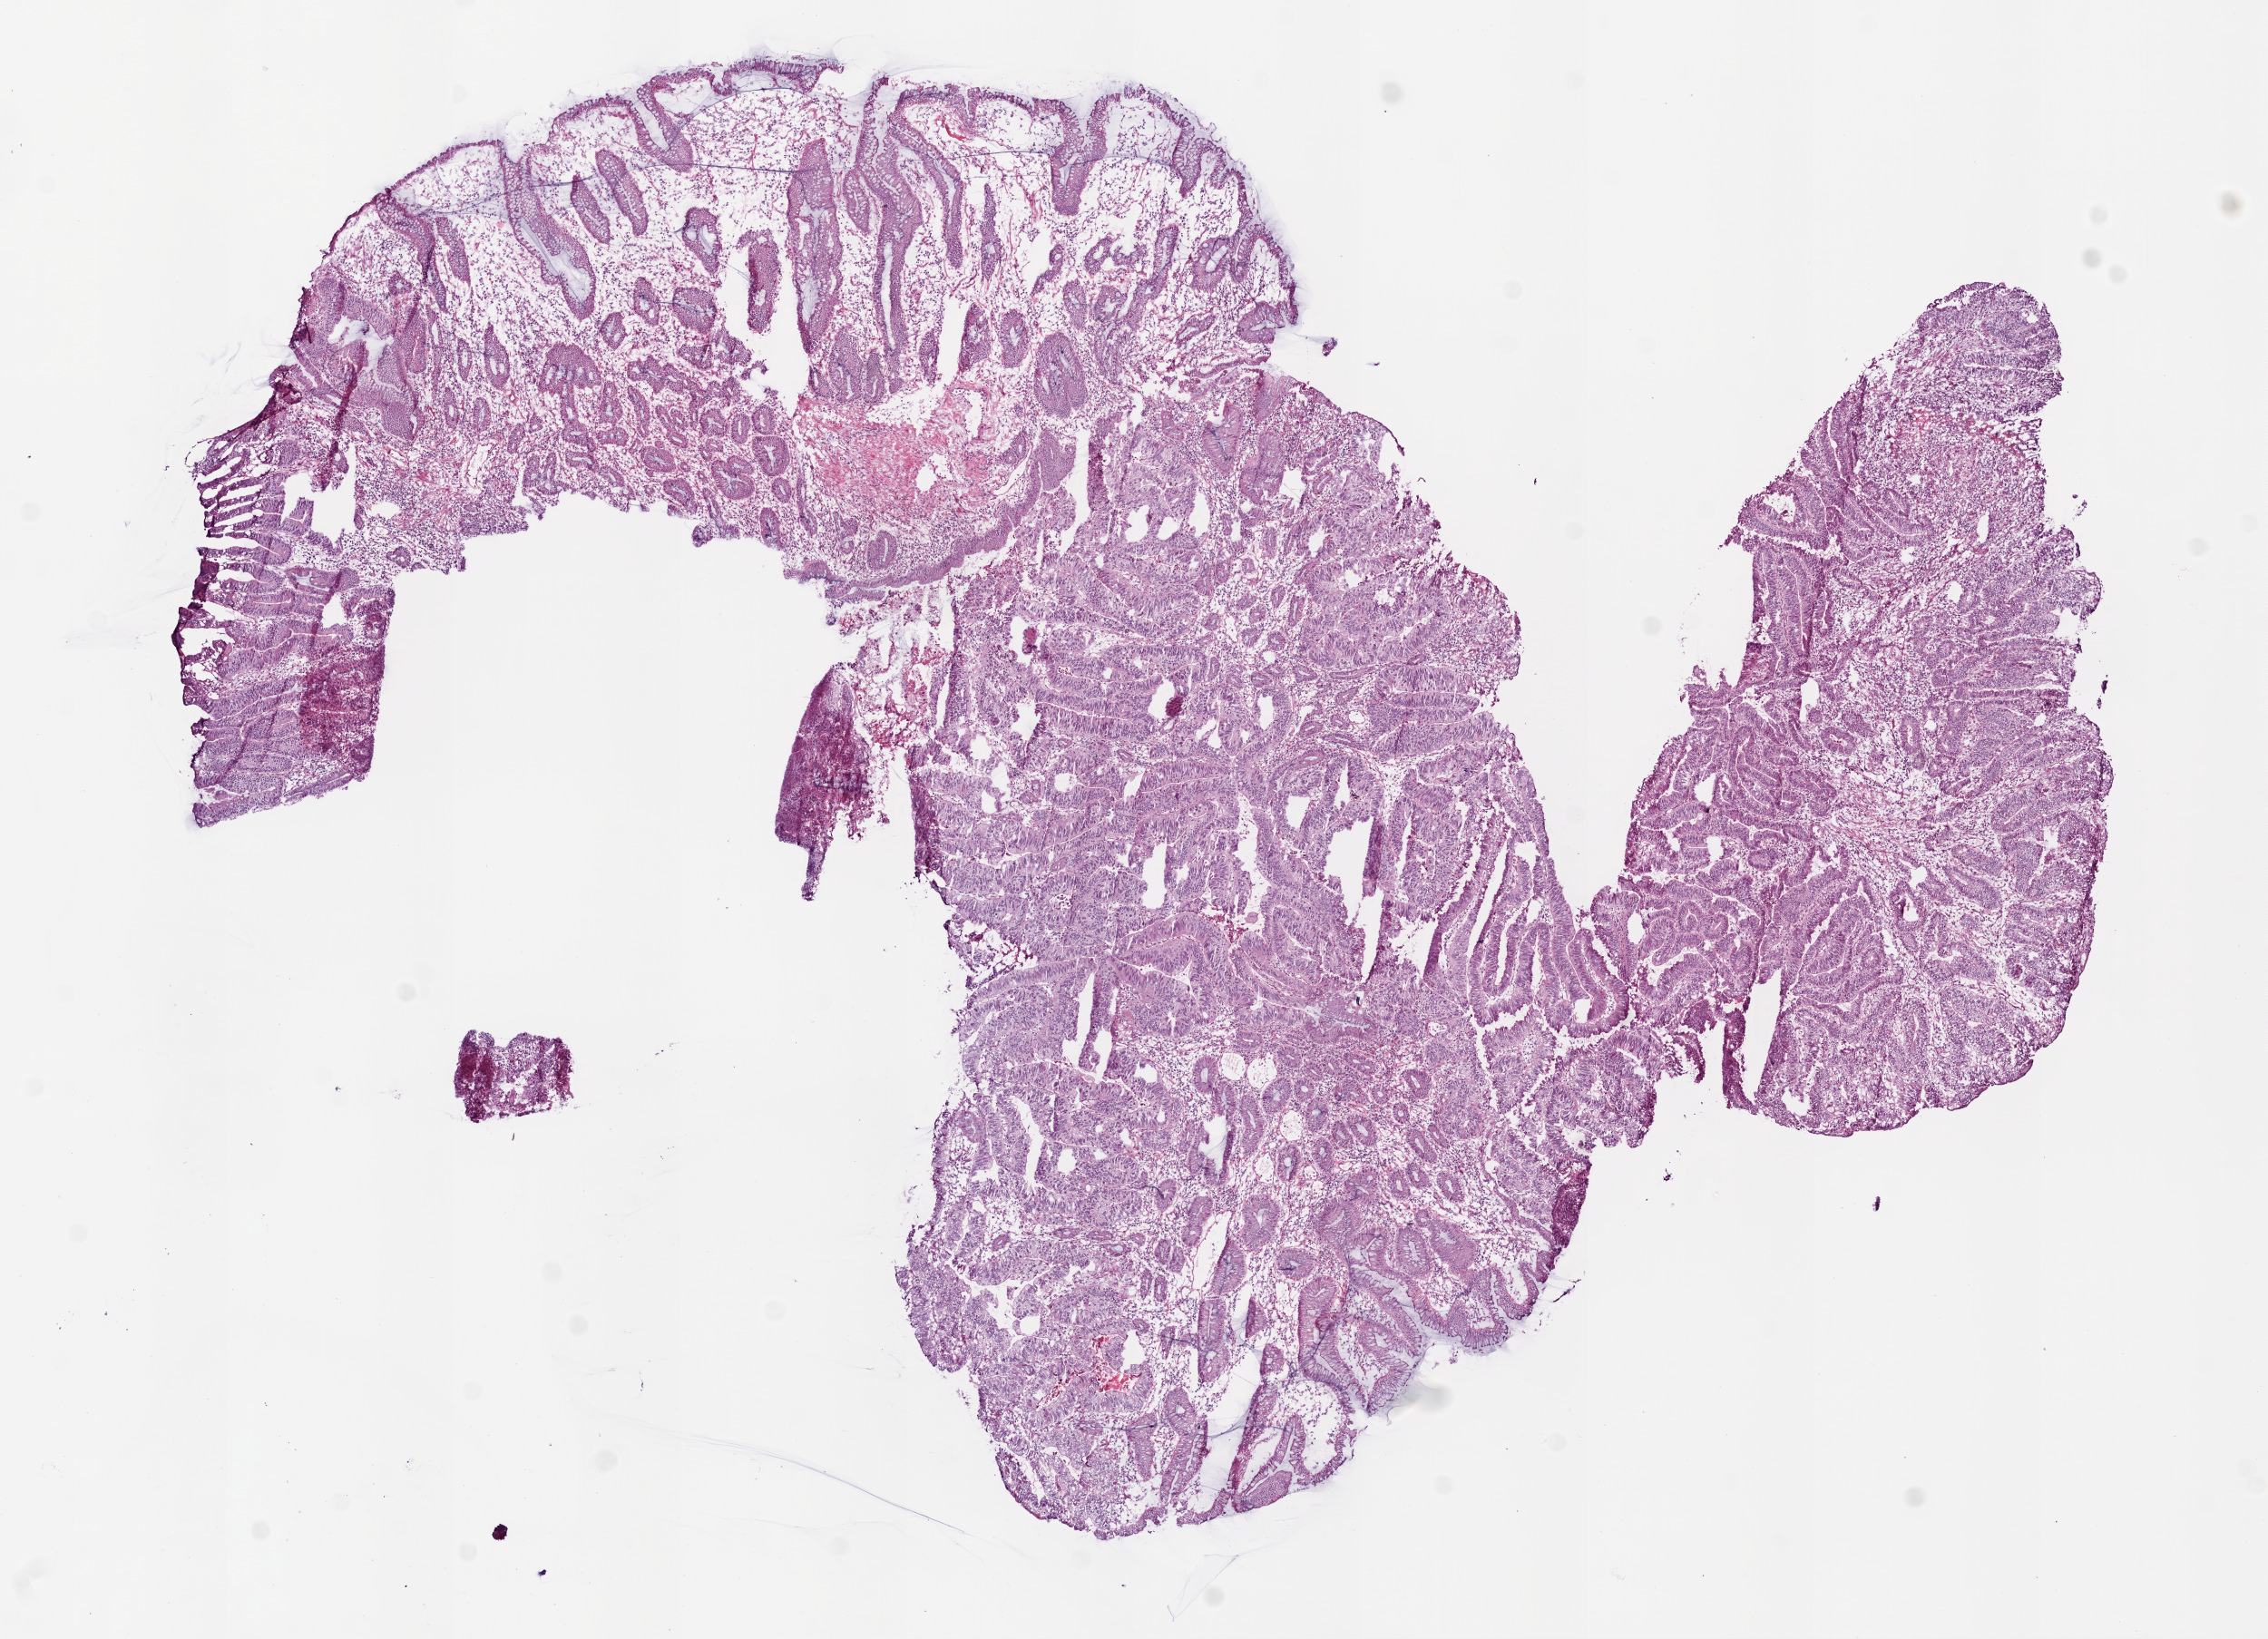
Digitized H&E-stained tissue section (whole slide), shown as a low-resolution overview of the whole scanned area (about 10.0 x 7.2 mm). Frozen section from the bottom of the tissue portion. Sample: primary tumour, colon. Patient: male, age at initial diagnosis 72 years.
Diagnosis: Adenocarcinoma, NOS.